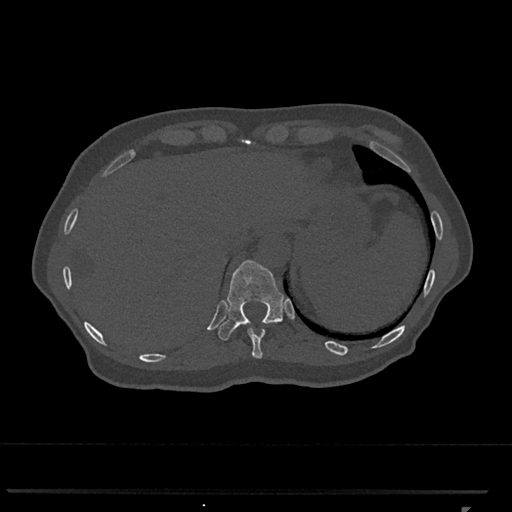
CT including the spine, one axial slice; position 536 of 793 along the scan axis; bone window (W 1800 / L 400 HU); 0.5 mm slice thickness; 512 × 512 image matrix, field of view 380 × 380 mm. Female patient, age 62 years. Case-level facts recorded for this patient, not image findings: primary cancer: renal.
Structures marked on this image (semi-automatic segmentation, software-assisted and operator-edited):
- T10 vertebra: bounding box <248,328,265,359> (left, top, right, bottom; pixels)
- T11 vertebra: <218,260,284,341>